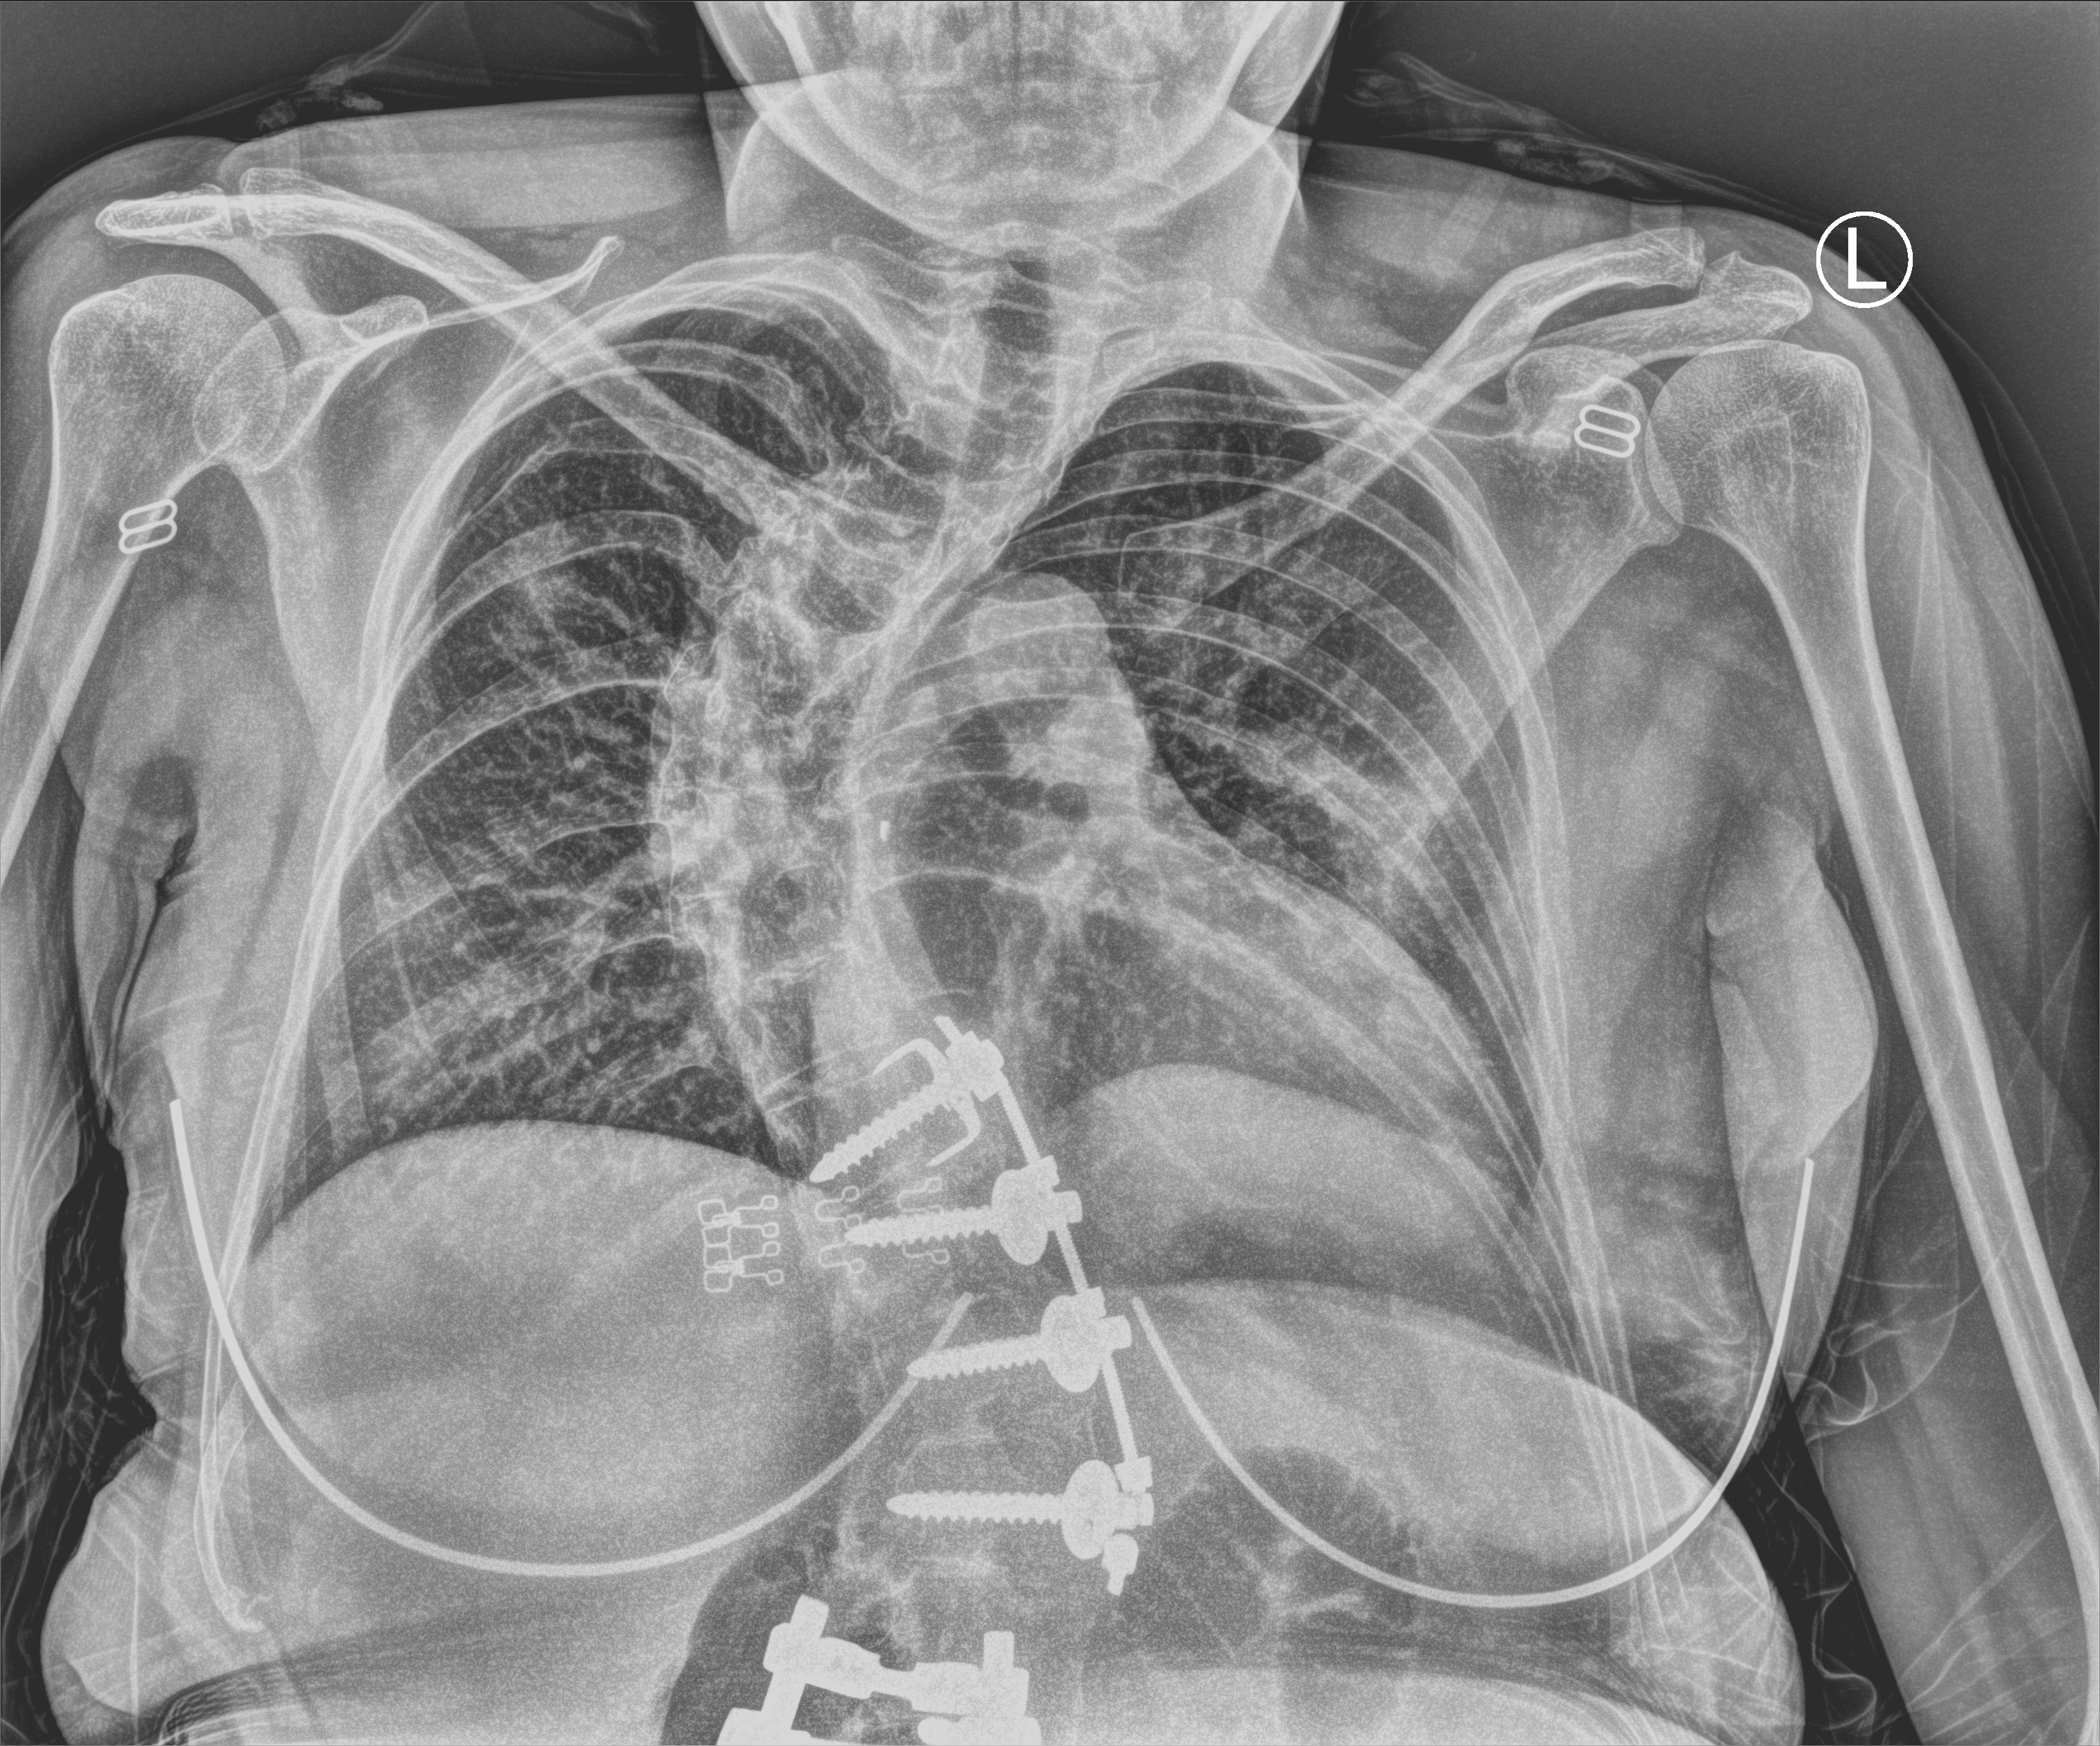
Chest X-ray (portable); anteroposterior (AP) projection. Female patient hospitalised with COVID-19, age 18–59 years.
Admission-level facts for this patient (not findings on this image; timing relative to this image not recorded):
- length of hospital stay: 3 days